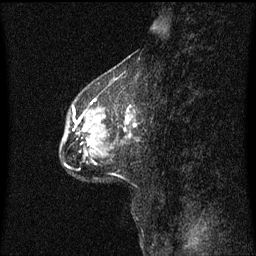
Breast MRI (dynamic contrast-enhanced), one sagittal slice; slice 20 of 60 in the series (ordered by position); dynamic contrast-enhanced series, image 2 of 3 at this slice position (ordered by acquisition); 1.5 T; TE 4.2 ms, TR 8.4 ms; 2 mm slice thickness; 256 × 256 image matrix, field of view 200 × 200 mm. Female patient, age 49 years. From the clinical record (not read from this slice): setting: breast cancer imaged before/during neoadjuvant chemotherapy; receptor status: HR-positive, HER2-negative.
Structures marked on this image (semi-automatic segmentation, software-assisted and operator-edited):
- analysis volume of interest (the breast-tissue region the enhancement analysis was run in; not a lesion): box from (x=61, y=106) to (x=136, y=158) px
- tumour enhancement mask (voxels above the 70 % enhancement threshold inside the analysis volume of interest): (x=88, y=118)–(x=129, y=145)